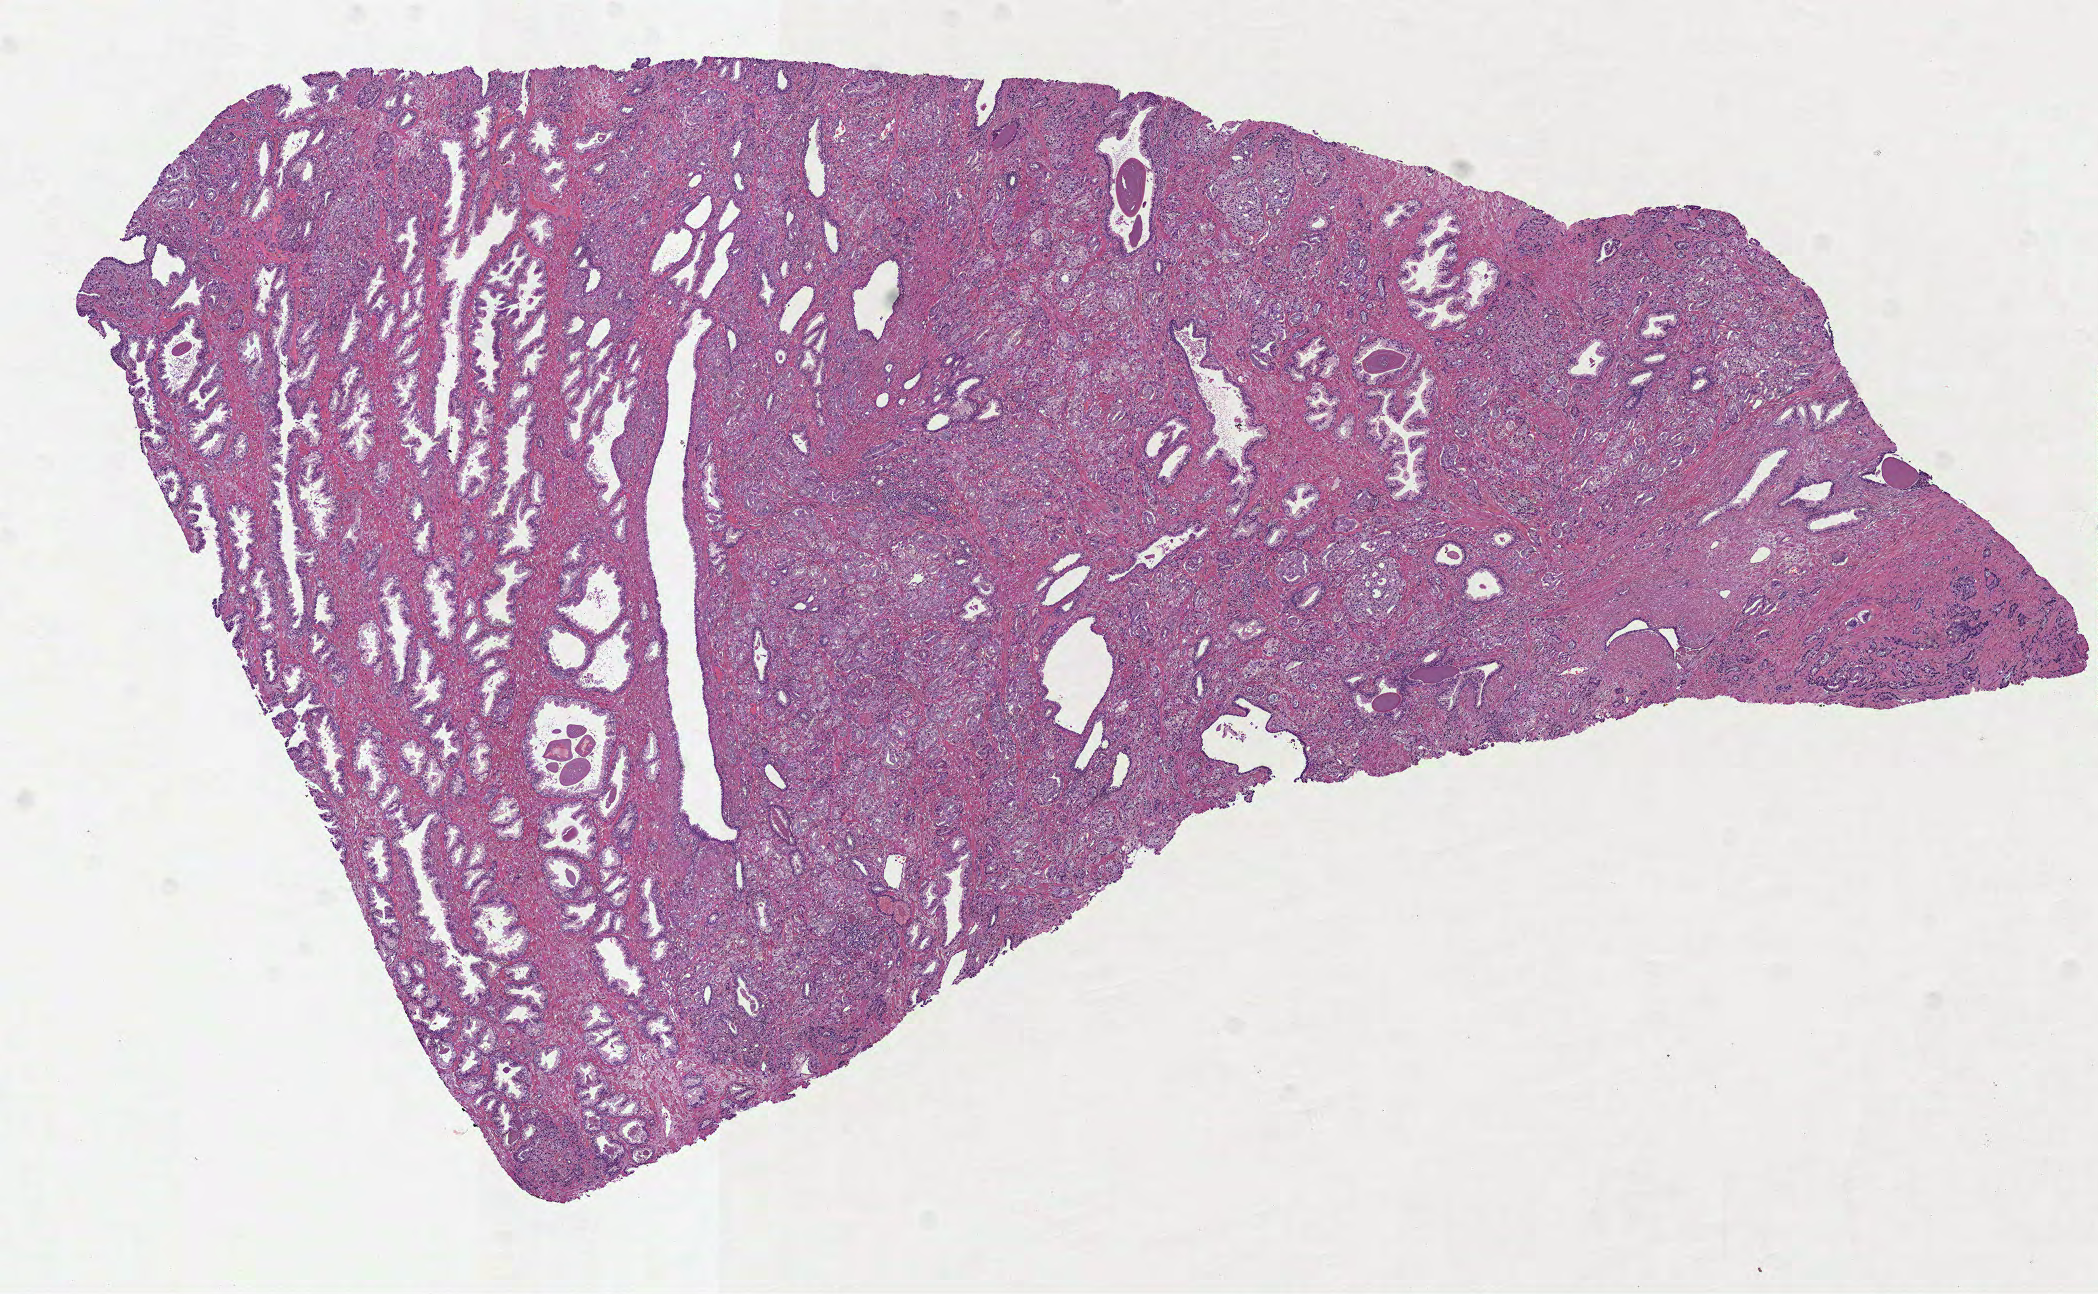
Hematoxylin and eosin (H&E) stained whole-slide image — whole scanned area (about 8.5 x 5.2 mm) shown as a low-resolution overview; FFPE section; sample: primary tumour, prostate. Male patient; age at initial diagnosis 70 years. Gleason score: 7 (4+3).
• diagnosis: Acinar cell carcinoma (prostate gland)
• laterality: right
• lymph nodes positive (case pathology): 0 of 10 examined